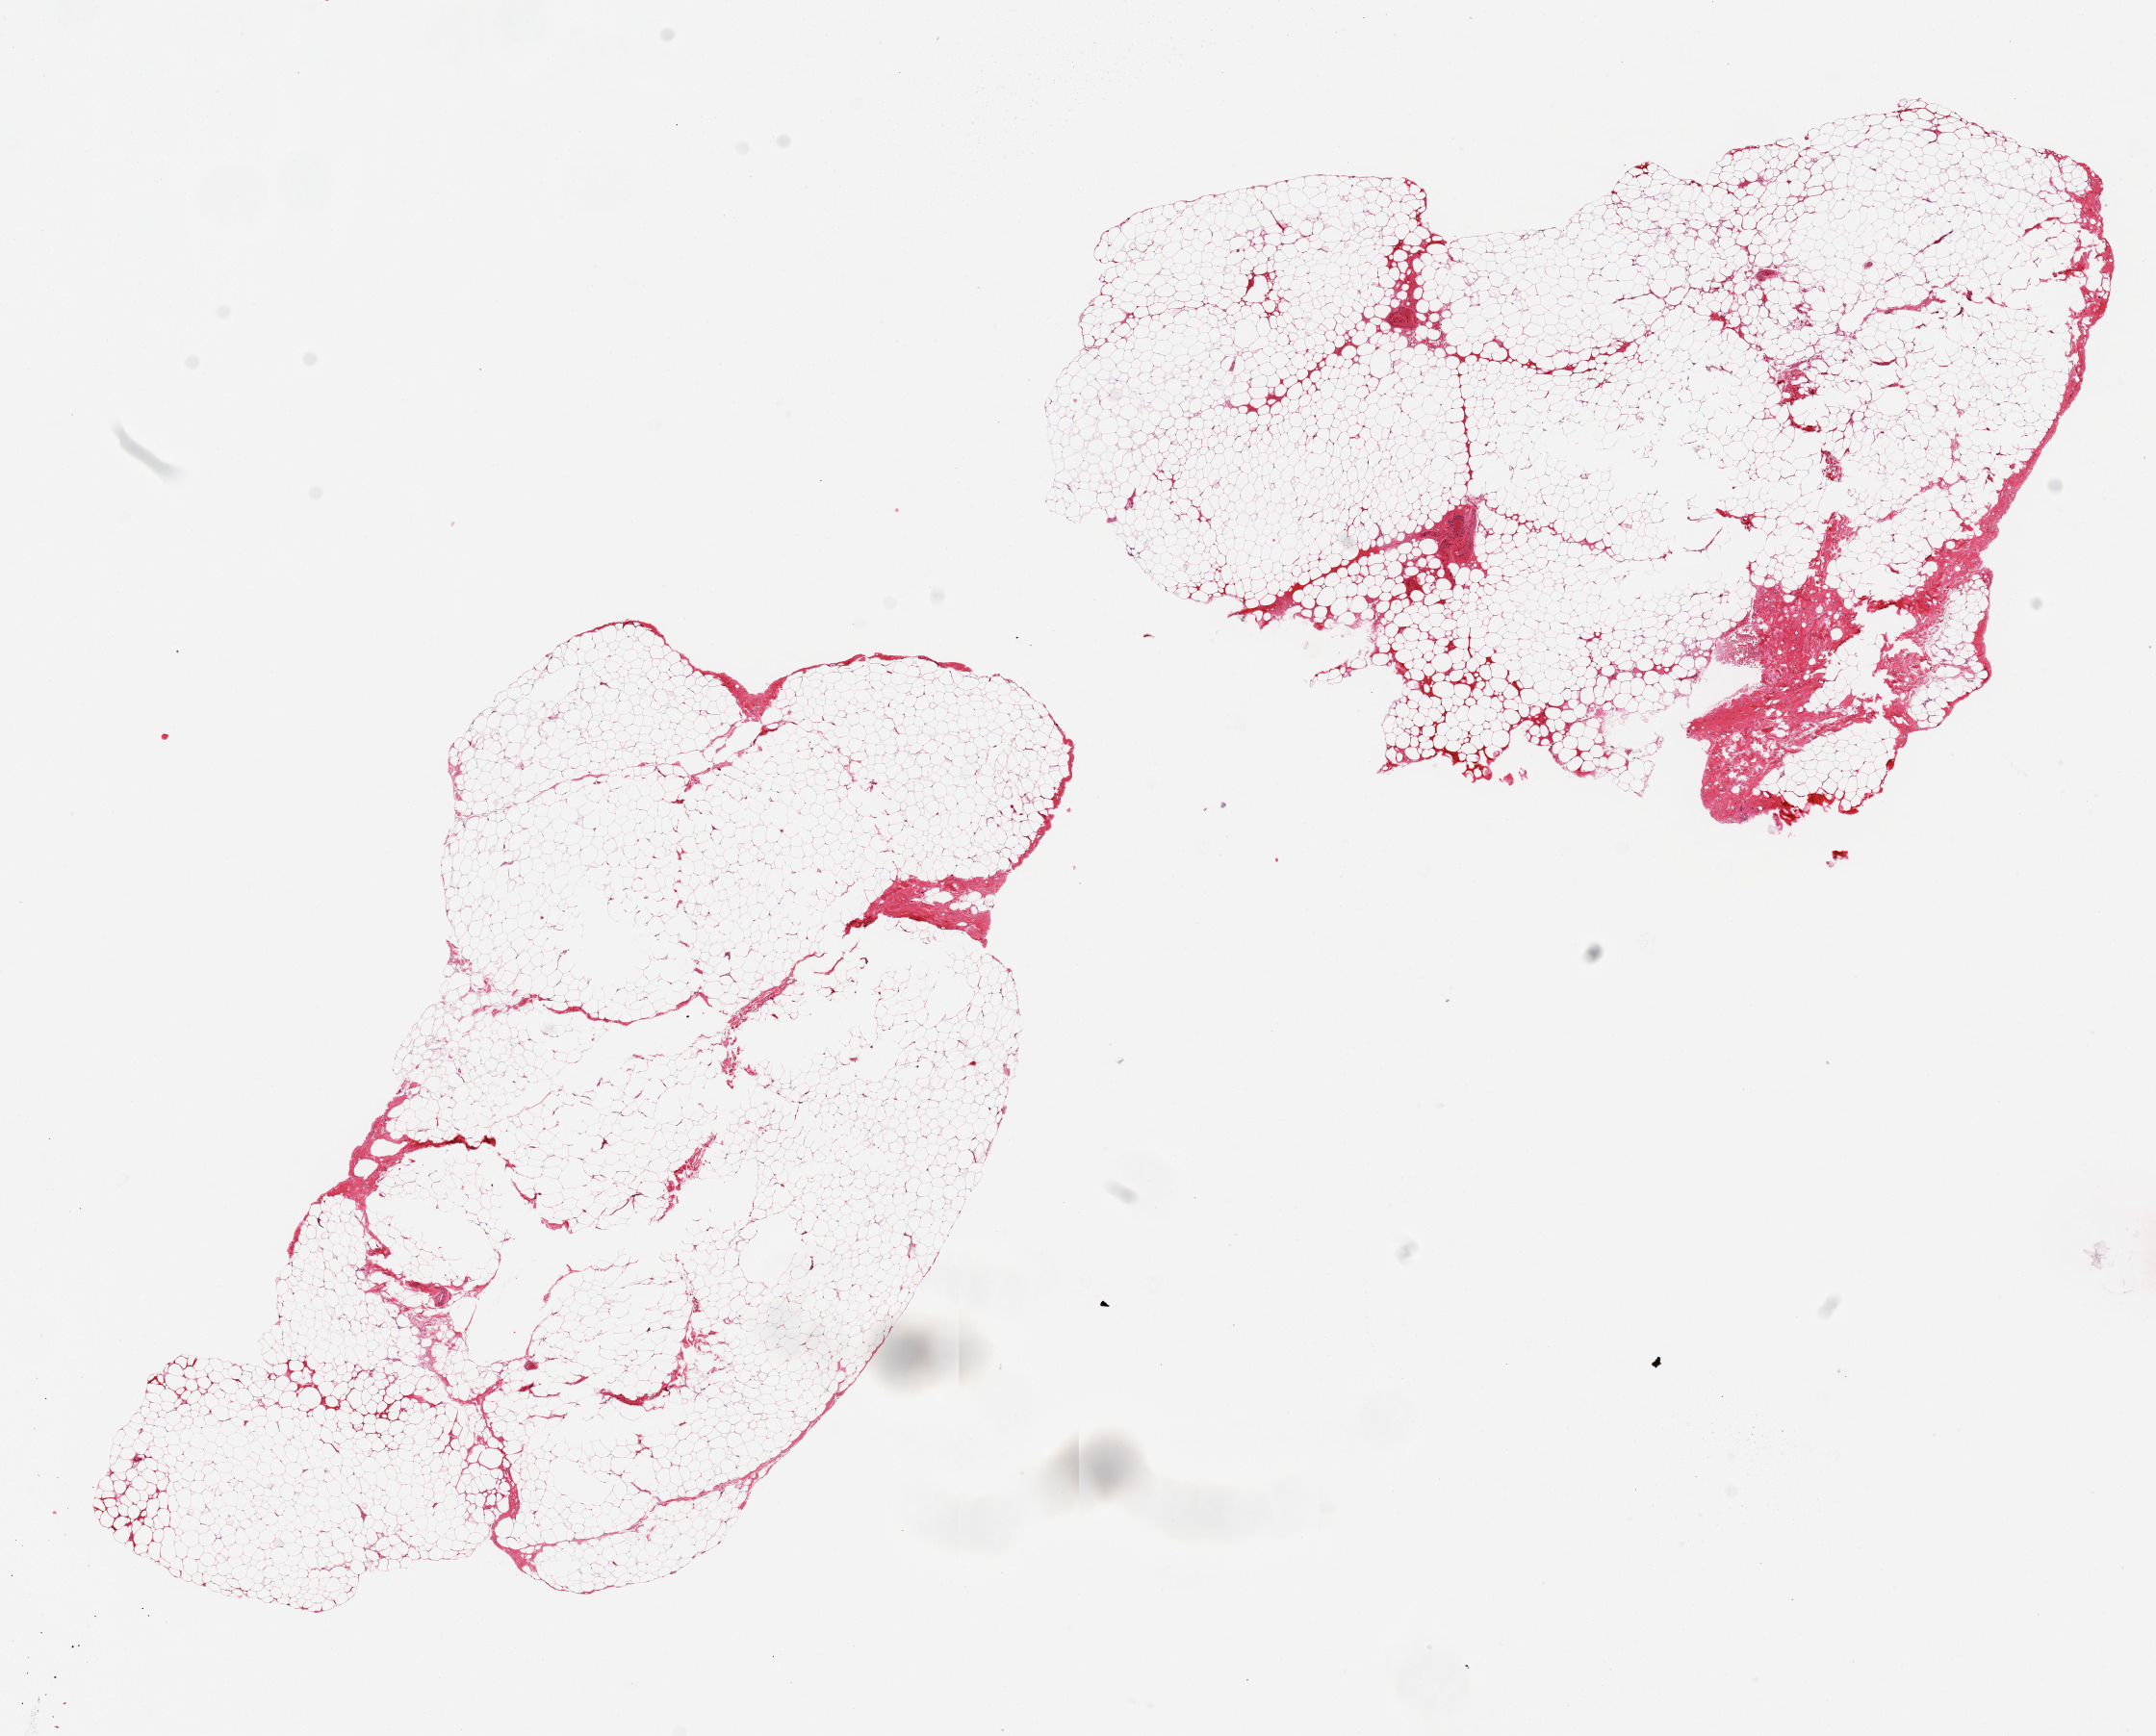
H&E whole-slide image — low-resolution overview of the scanned area, about 17.7 x 14.3 mm (slide scanned at 20x). PAXgene-fixed, paraffin-embedded tissue. Target tissue: breast. Tissue donor sample. Male donor.
Pathologist's review note for this sample: 2 pieces ~8x6mm. No ductal elements noted.